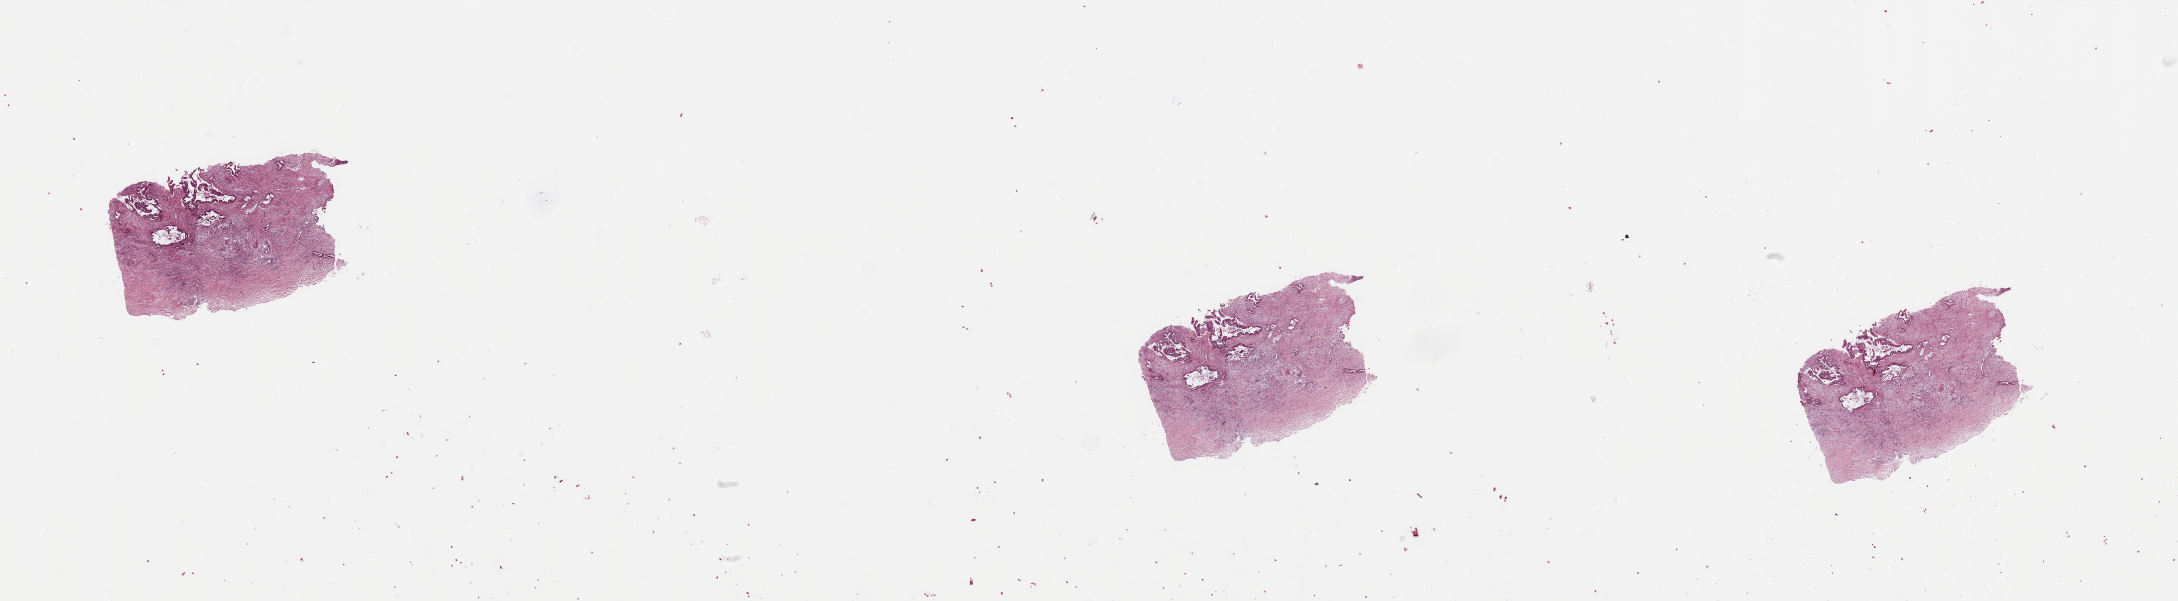
Whole-slide histology image, H&E — a low-resolution overview of the entire scanned area, about 34.5 x 9.5 mm, tumour tissue sample, sampled site: pancreas. Female, 70 y/o. Histologic grade: G2 (moderately differentiated). Pathologist review of this section (percent, as recorded): tumour nuclei 20%, necrosis 2%.
* AJCC pathologic stage: IIB
* diagnosis: Infiltrating duct carcinoma, NOS
* primary tumour site (as recorded): head